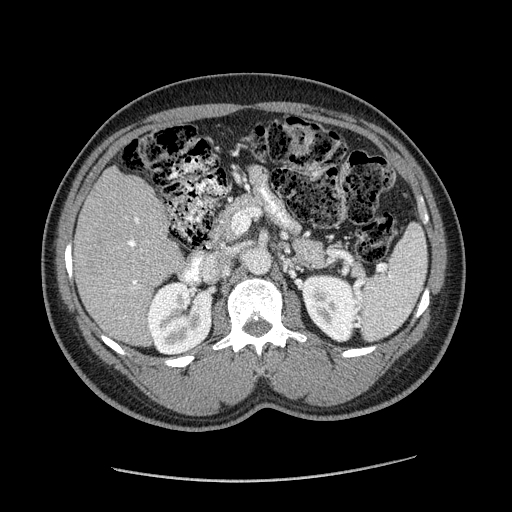
Contrast-enhanced abdominal CT (liver protocol), one axial slice. Slice 83 of 182 in the series (ordered by position). Reconstruction kernel STANDARD. Soft-tissue window (W 400 / L 40 HU). 512 × 512 image matrix. From the clinical record (not read from this slice): diagnosis: hepatocellular carcinoma (patient treated with transarterial chemoembolisation; whether this scan precedes or follows treatment is not stated here); TNM stage (as recorded): Stage-I; Child-Pugh class: A; tumour nodularity: uninodular; tumour size: 3.1 cm.
Annotated regions visible in this slice (semi-automatically segmented with operator editing):
- liver parenchyma outside the tumour (the mass and vessels are separate outlines, so this box may not span the whole liver): bounding box <74,166,182,346> (left, top, right, bottom; pixels)
- liver vessels: <128,217,139,284>